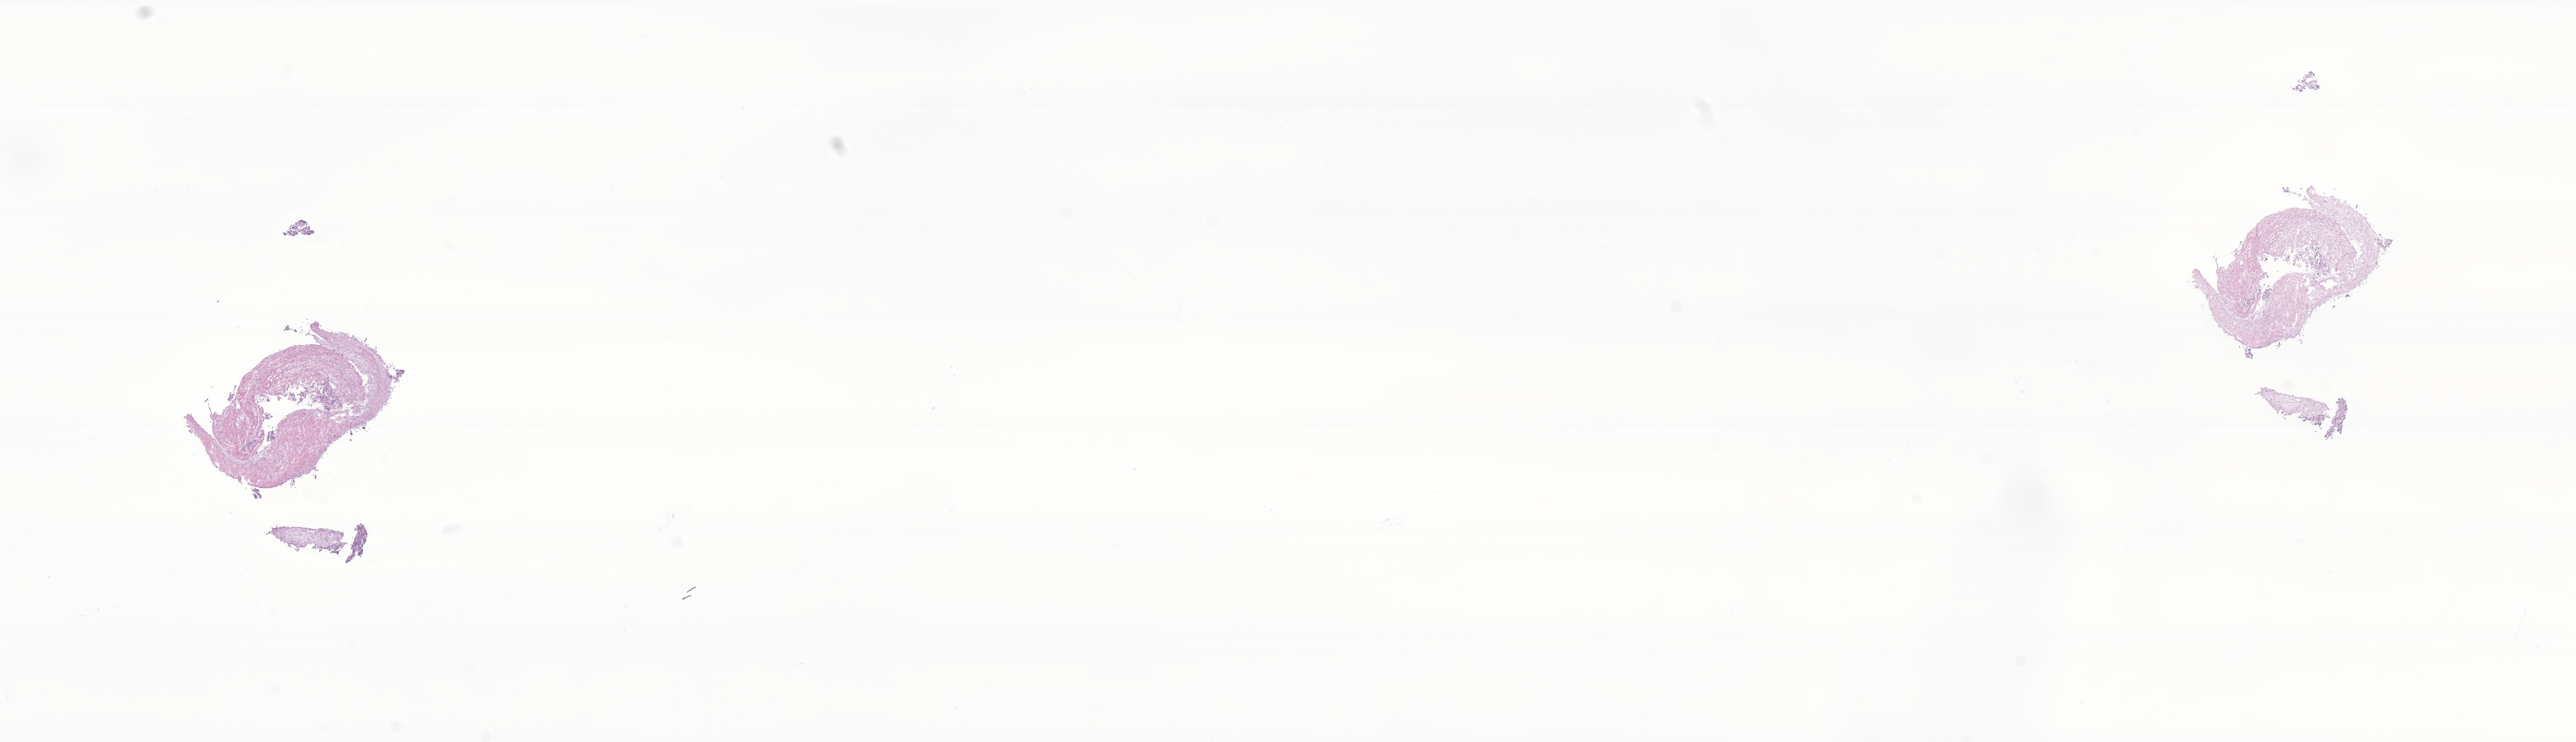
Whole-slide image, H&E stain of tumor tissue from the spinal cord, low-resolution overview of the scanned area, about 25.8 x 7.4 mm, cryosection (OCT / tissue freezing medium). Male patient, age 53 months.
Diagnosis (ICD-O-3 morphology term): Neoplasm, uncertain whether benign or malignant.